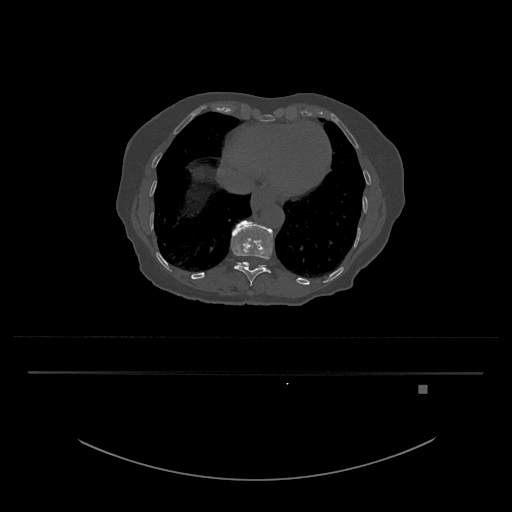
CT including the spine, one axial slice; reconstruction kernel Br40s/3; 120 kVp; bone window (W 1800 / L 400 HU); 0.5 mm slice thickness; 512 × 512 image matrix, field of view 500 × 500 mm. Female patient, age 57 years. Case-level facts recorded for this patient, not image findings: primary cancer: cervical.
Annotated regions visible in this slice (semi-automatically segmented with operator editing):
- T11 vertebra: bounding box (x1, y1, x2, y2) in pixels: (231, 220, 273, 286)
- T12 vertebra: (236, 262, 266, 268)